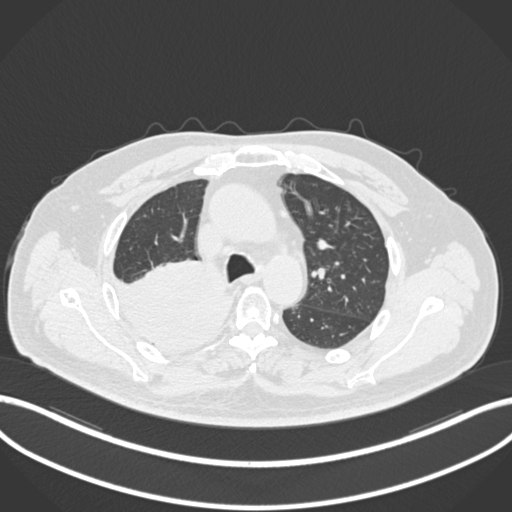
Chest CT, one axial slice; slice 144 of 218 in the series (ordered by position); reconstruction kernel B30f; lung window (W 1500 / L -600 HU); 1 mm slice thickness; 512 × 512 image matrix, field of view 400 × 400 mm. Patient: male, 68 years. Case-level facts recorded for this patient, not image findings: clinical TNM (as recorded): T2a N0 M0.
Outlined on this slice (rectangle marked by the reading radiologist):
- lung tumour (recorded histology: adenocarcinoma): box from (x=115, y=261) to (x=237, y=360) px